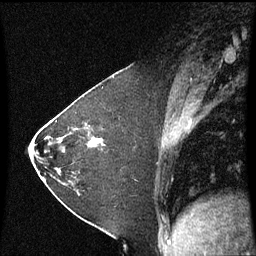
Breast MRI (dynamic contrast-enhanced), one sagittal slice; slice 30 of 60 in the series (ordered by position); dynamic contrast-enhanced series, image 2 of 3 at this slice position (ordered by acquisition); 1.5 T; TE 4.2 ms, TR 8.9 ms; 2 mm slice thickness; 256 × 256 image matrix, field of view 200 × 200 mm. Patient: female, 37 years. From the clinical record (not read from this slice): setting: breast cancer imaged before/during neoadjuvant chemotherapy; receptor status: HR-positive, HER2-negative.
Structures marked on this image (semi-automatic segmentation, software-assisted and operator-edited):
- analysis volume of interest (the breast-tissue region the enhancement analysis was run in; not a lesion): bounding box [x1, y1, x2, y2] px = [60, 102, 122, 181]
- tumour enhancement mask (voxels above the 70 % enhancement threshold inside the analysis volume of interest): [87, 124, 99, 147]